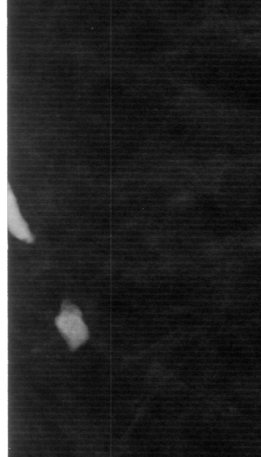
Cropped region of a digitized screen-film mammogram centred on a radiologist-marked abnormality; left breast; CC view.
- Calcifications, morphology lucent centered, distribution linear; BI-RADS assessment category 2; pathology result (as recorded, not read from the image): benign.